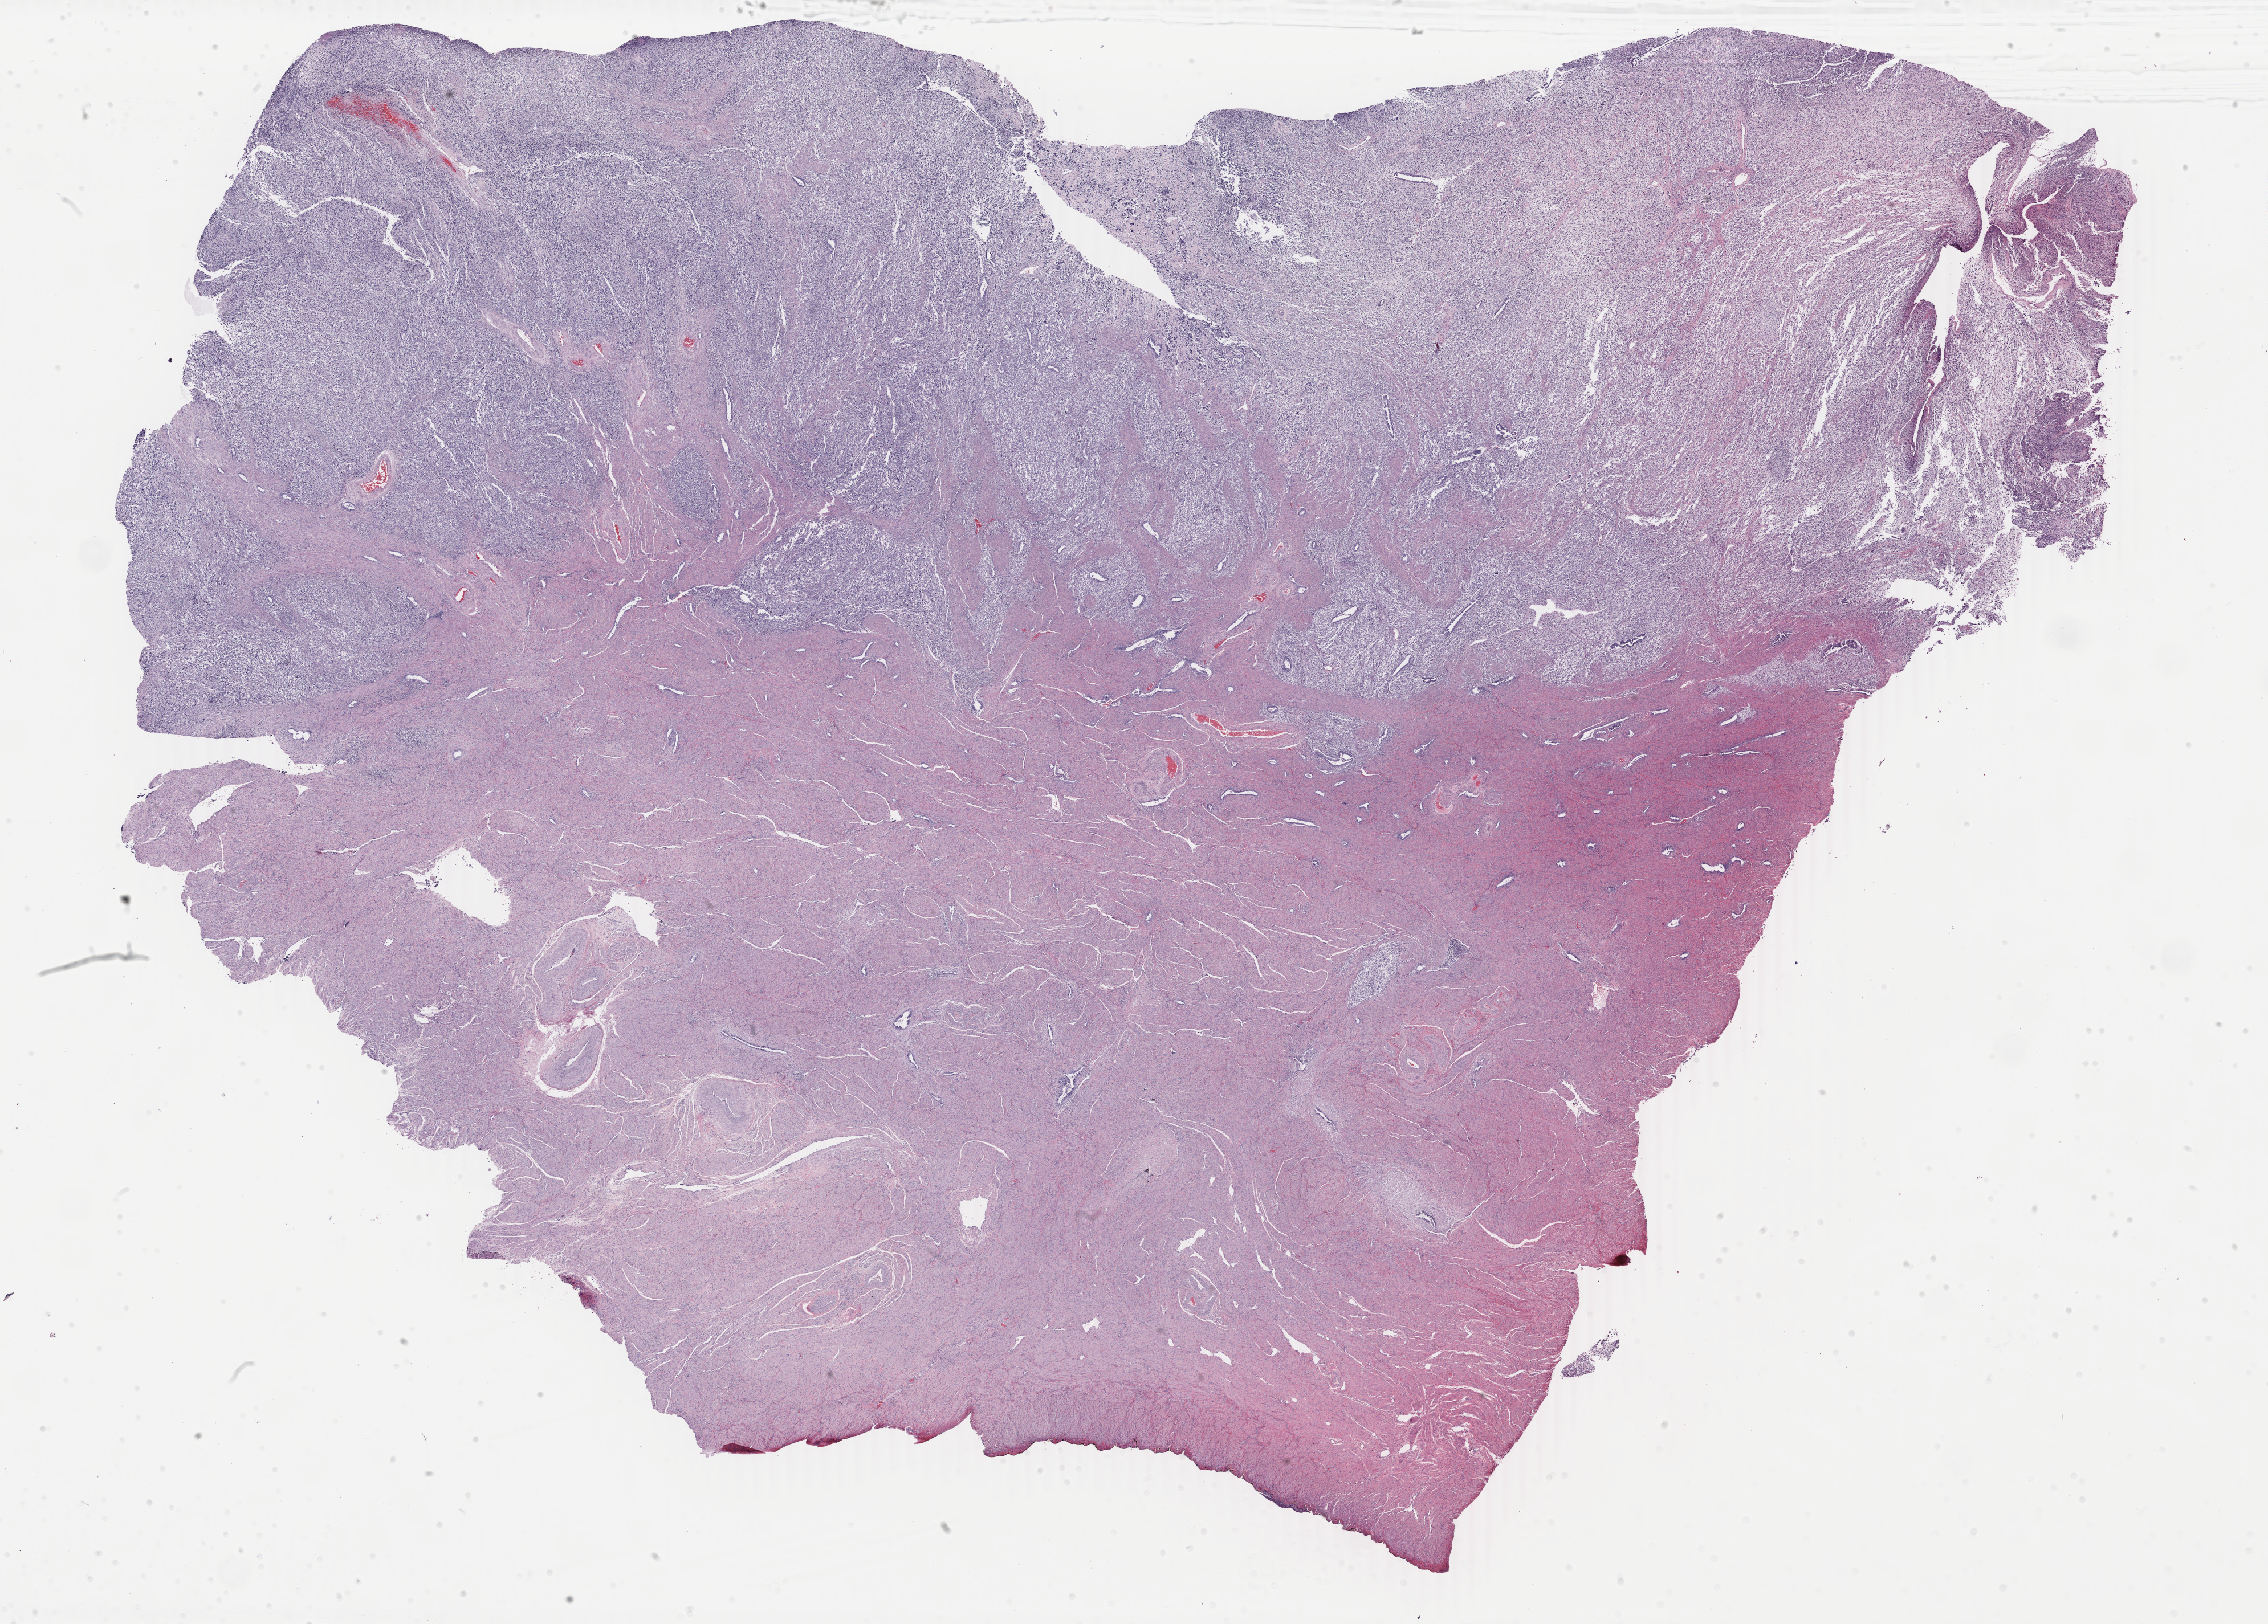
H&E whole-slide image — a low-resolution overview of the entire scanned area, about 31.6 x 22.7 mm (slide scanned at 40x); FFPE section; sample: primary tumour, uterus. Female patient; age at initial diagnosis 63 years.
FIGO stage: IIIC2. Pathologic diagnosis: Mullerian mixed tumor.